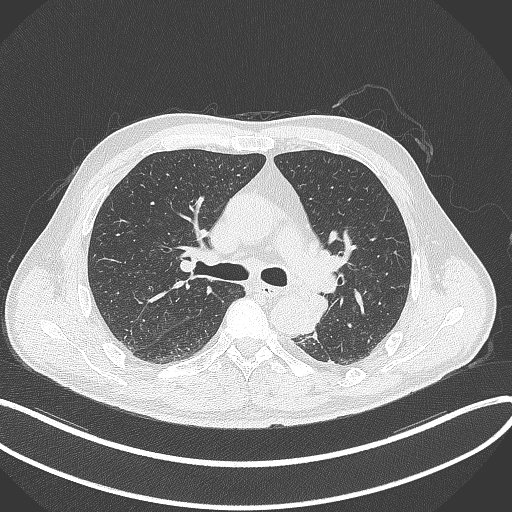
Chest CT, one axial slice; position 219 of 329 along the scan axis; 120 kVp; lung window (W 1500 / L -600 HU); 512 × 512 image matrix, field of view 400 × 400 mm. Male patient, age 59 years. From the clinical record (not read from this slice): clinical TNM (as recorded): T2a N2 M0.
Structures marked on this image (rectangle marked by the reading radiologist):
- lung tumour (recorded histology: squamous cell carcinoma): bounding box [x1, y1, x2, y2] px = [309, 292, 332, 327]